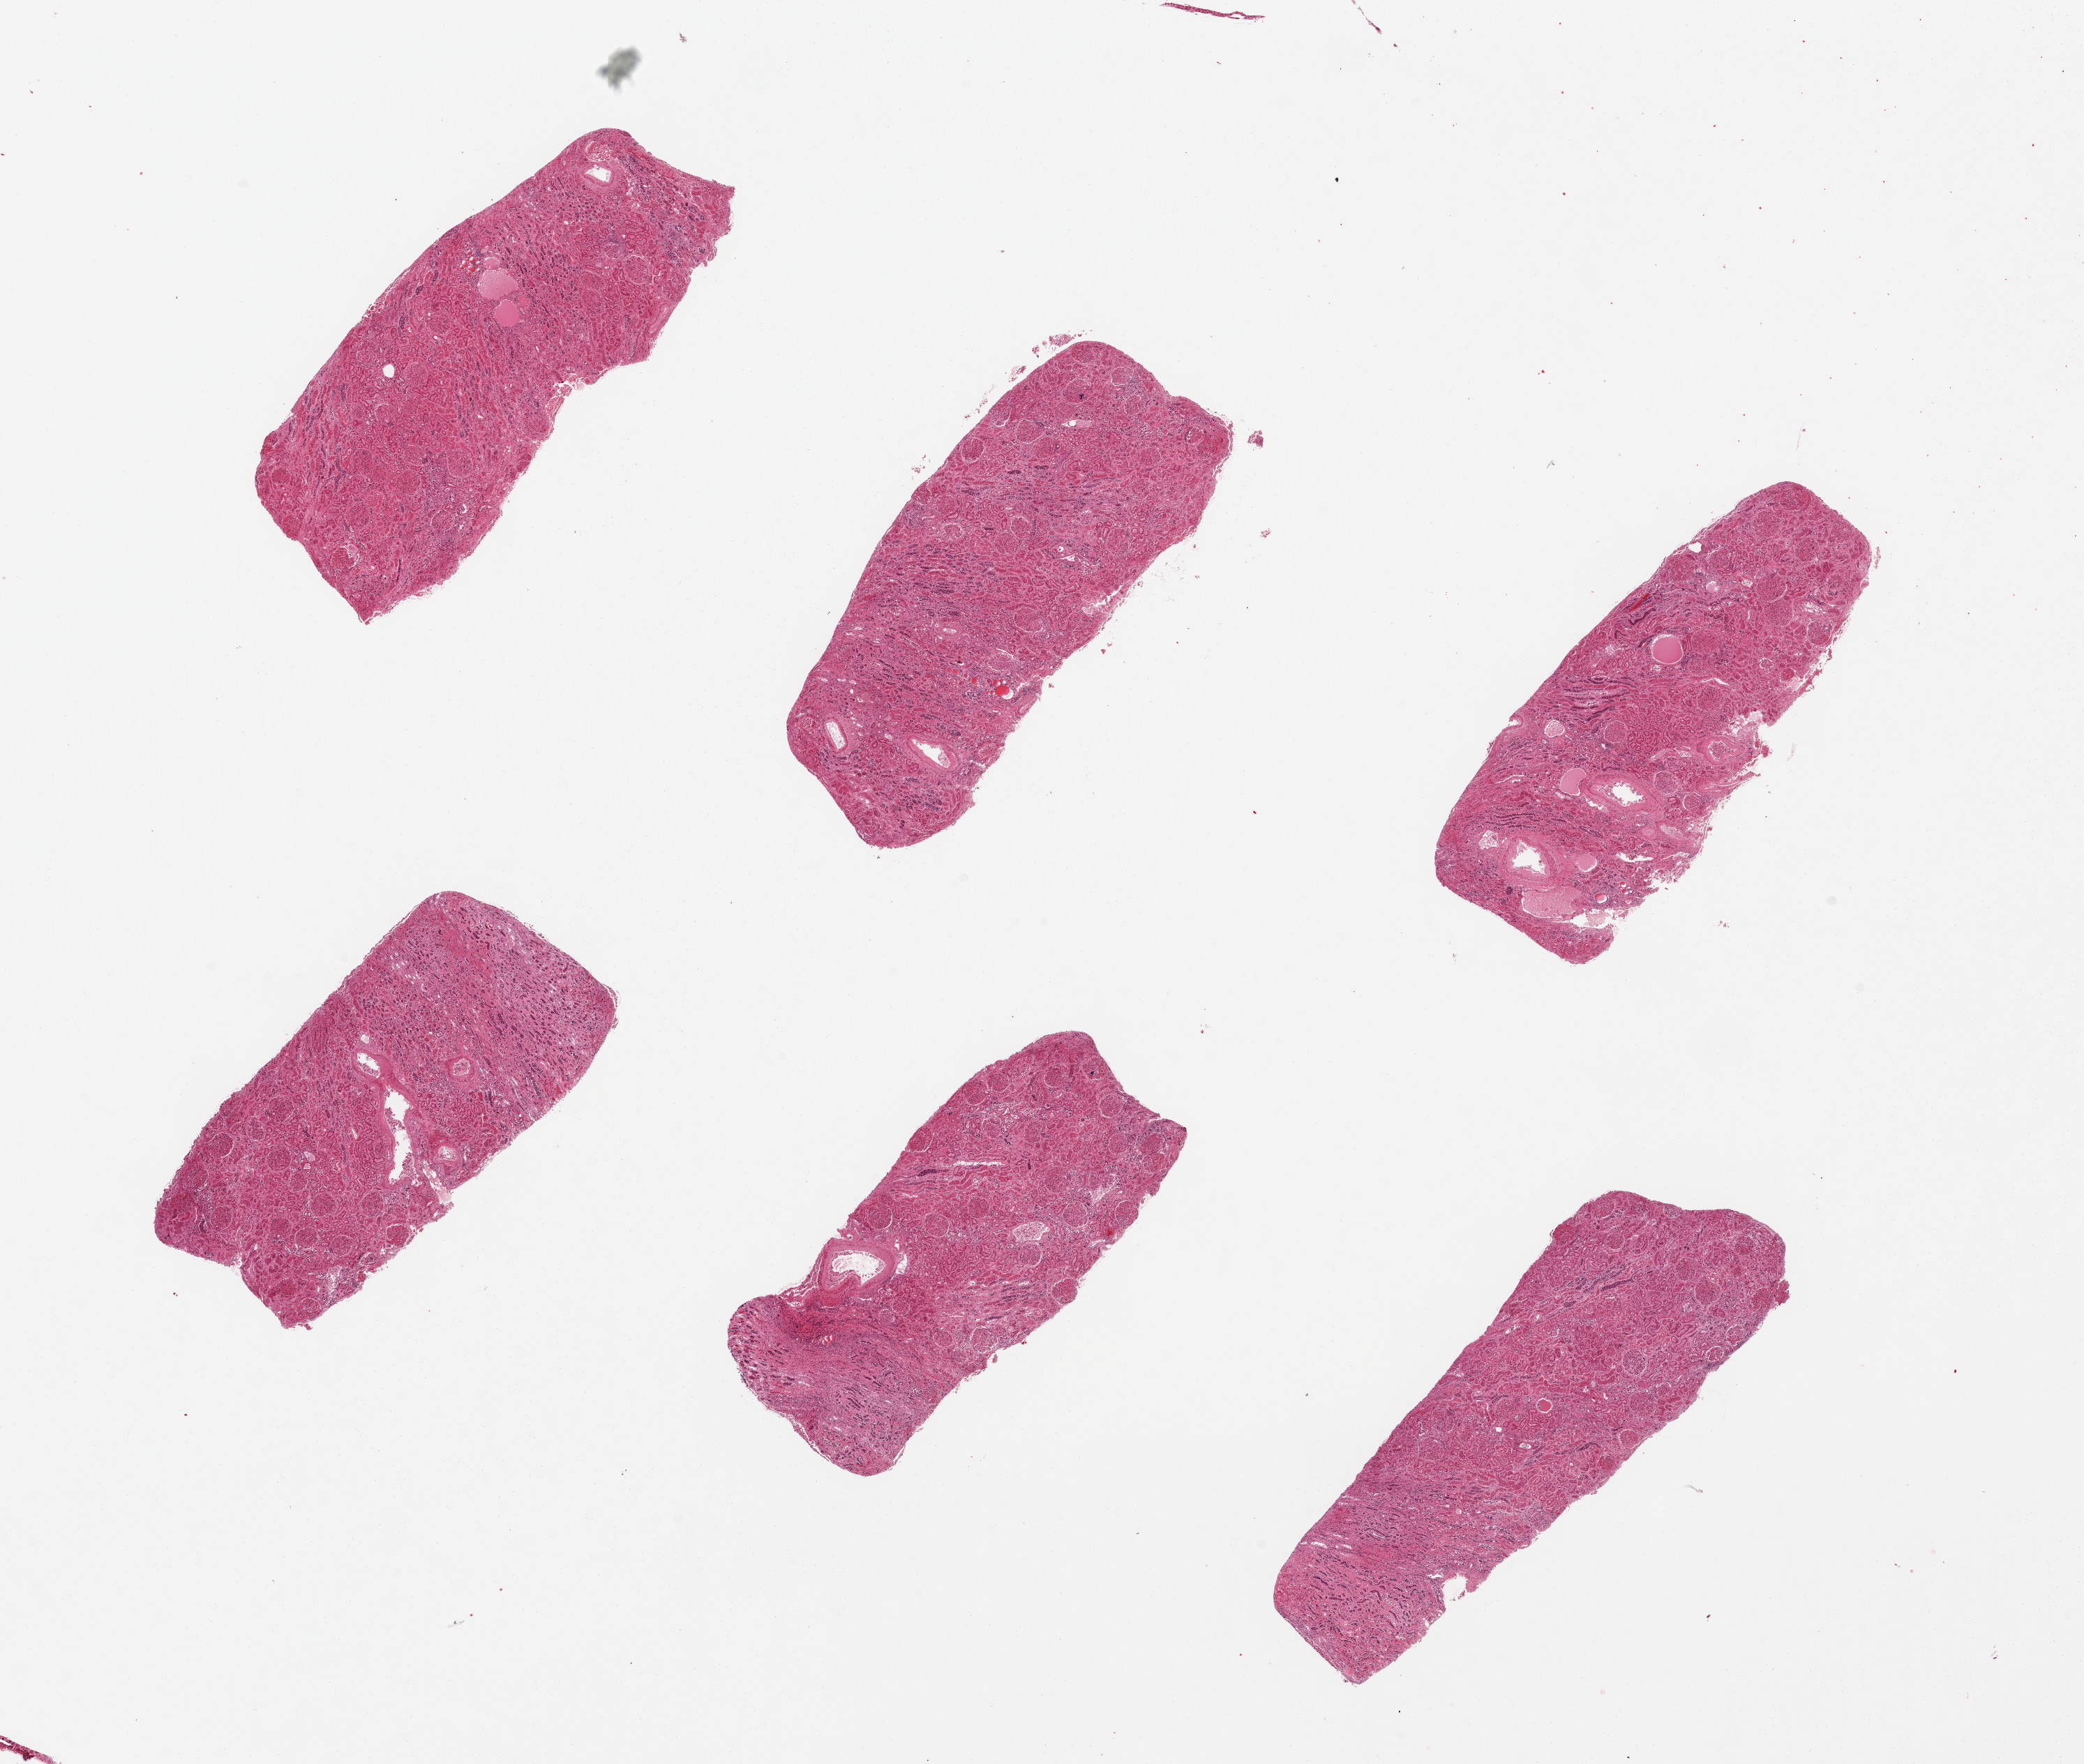
Digitized H&E-stained section, a low-resolution overview of the entire scanned area, about 23.6 x 20.0 mm; PAXgene-fixed paraffin-embedded (PFPE) section; target tissue: renal cortex; donor tissue sample. Donor: female.
Pathologist's review note for this sample: 6 pieces, glomeruli present in all sections; several are ~25% medulla.